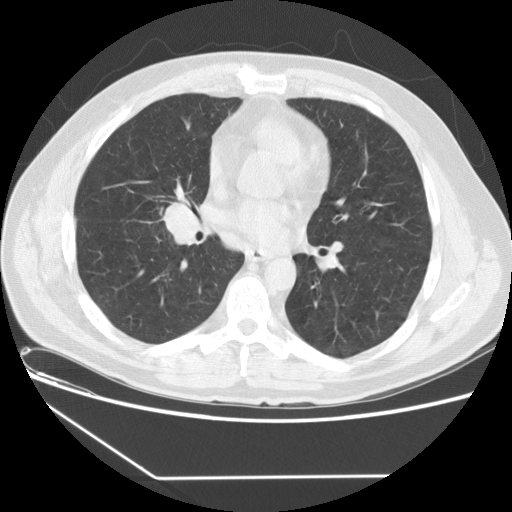
Low-dose screening chest CT, one axial slice. Slice 74 of 154 in the series (ordered by position). Reconstruction kernel STANDARD. 120 kVp. Lung window (W 1500 / L -600 HU). 2.5 mm slice thickness. 512 × 512 image matrix.
Annotated regions visible in this slice (manually delineated by an expert):
- lesion 1 (tumor, middle lobe of right lung): bounding box (x1, y1, x2, y2) in pixels: (165, 204, 199, 244)